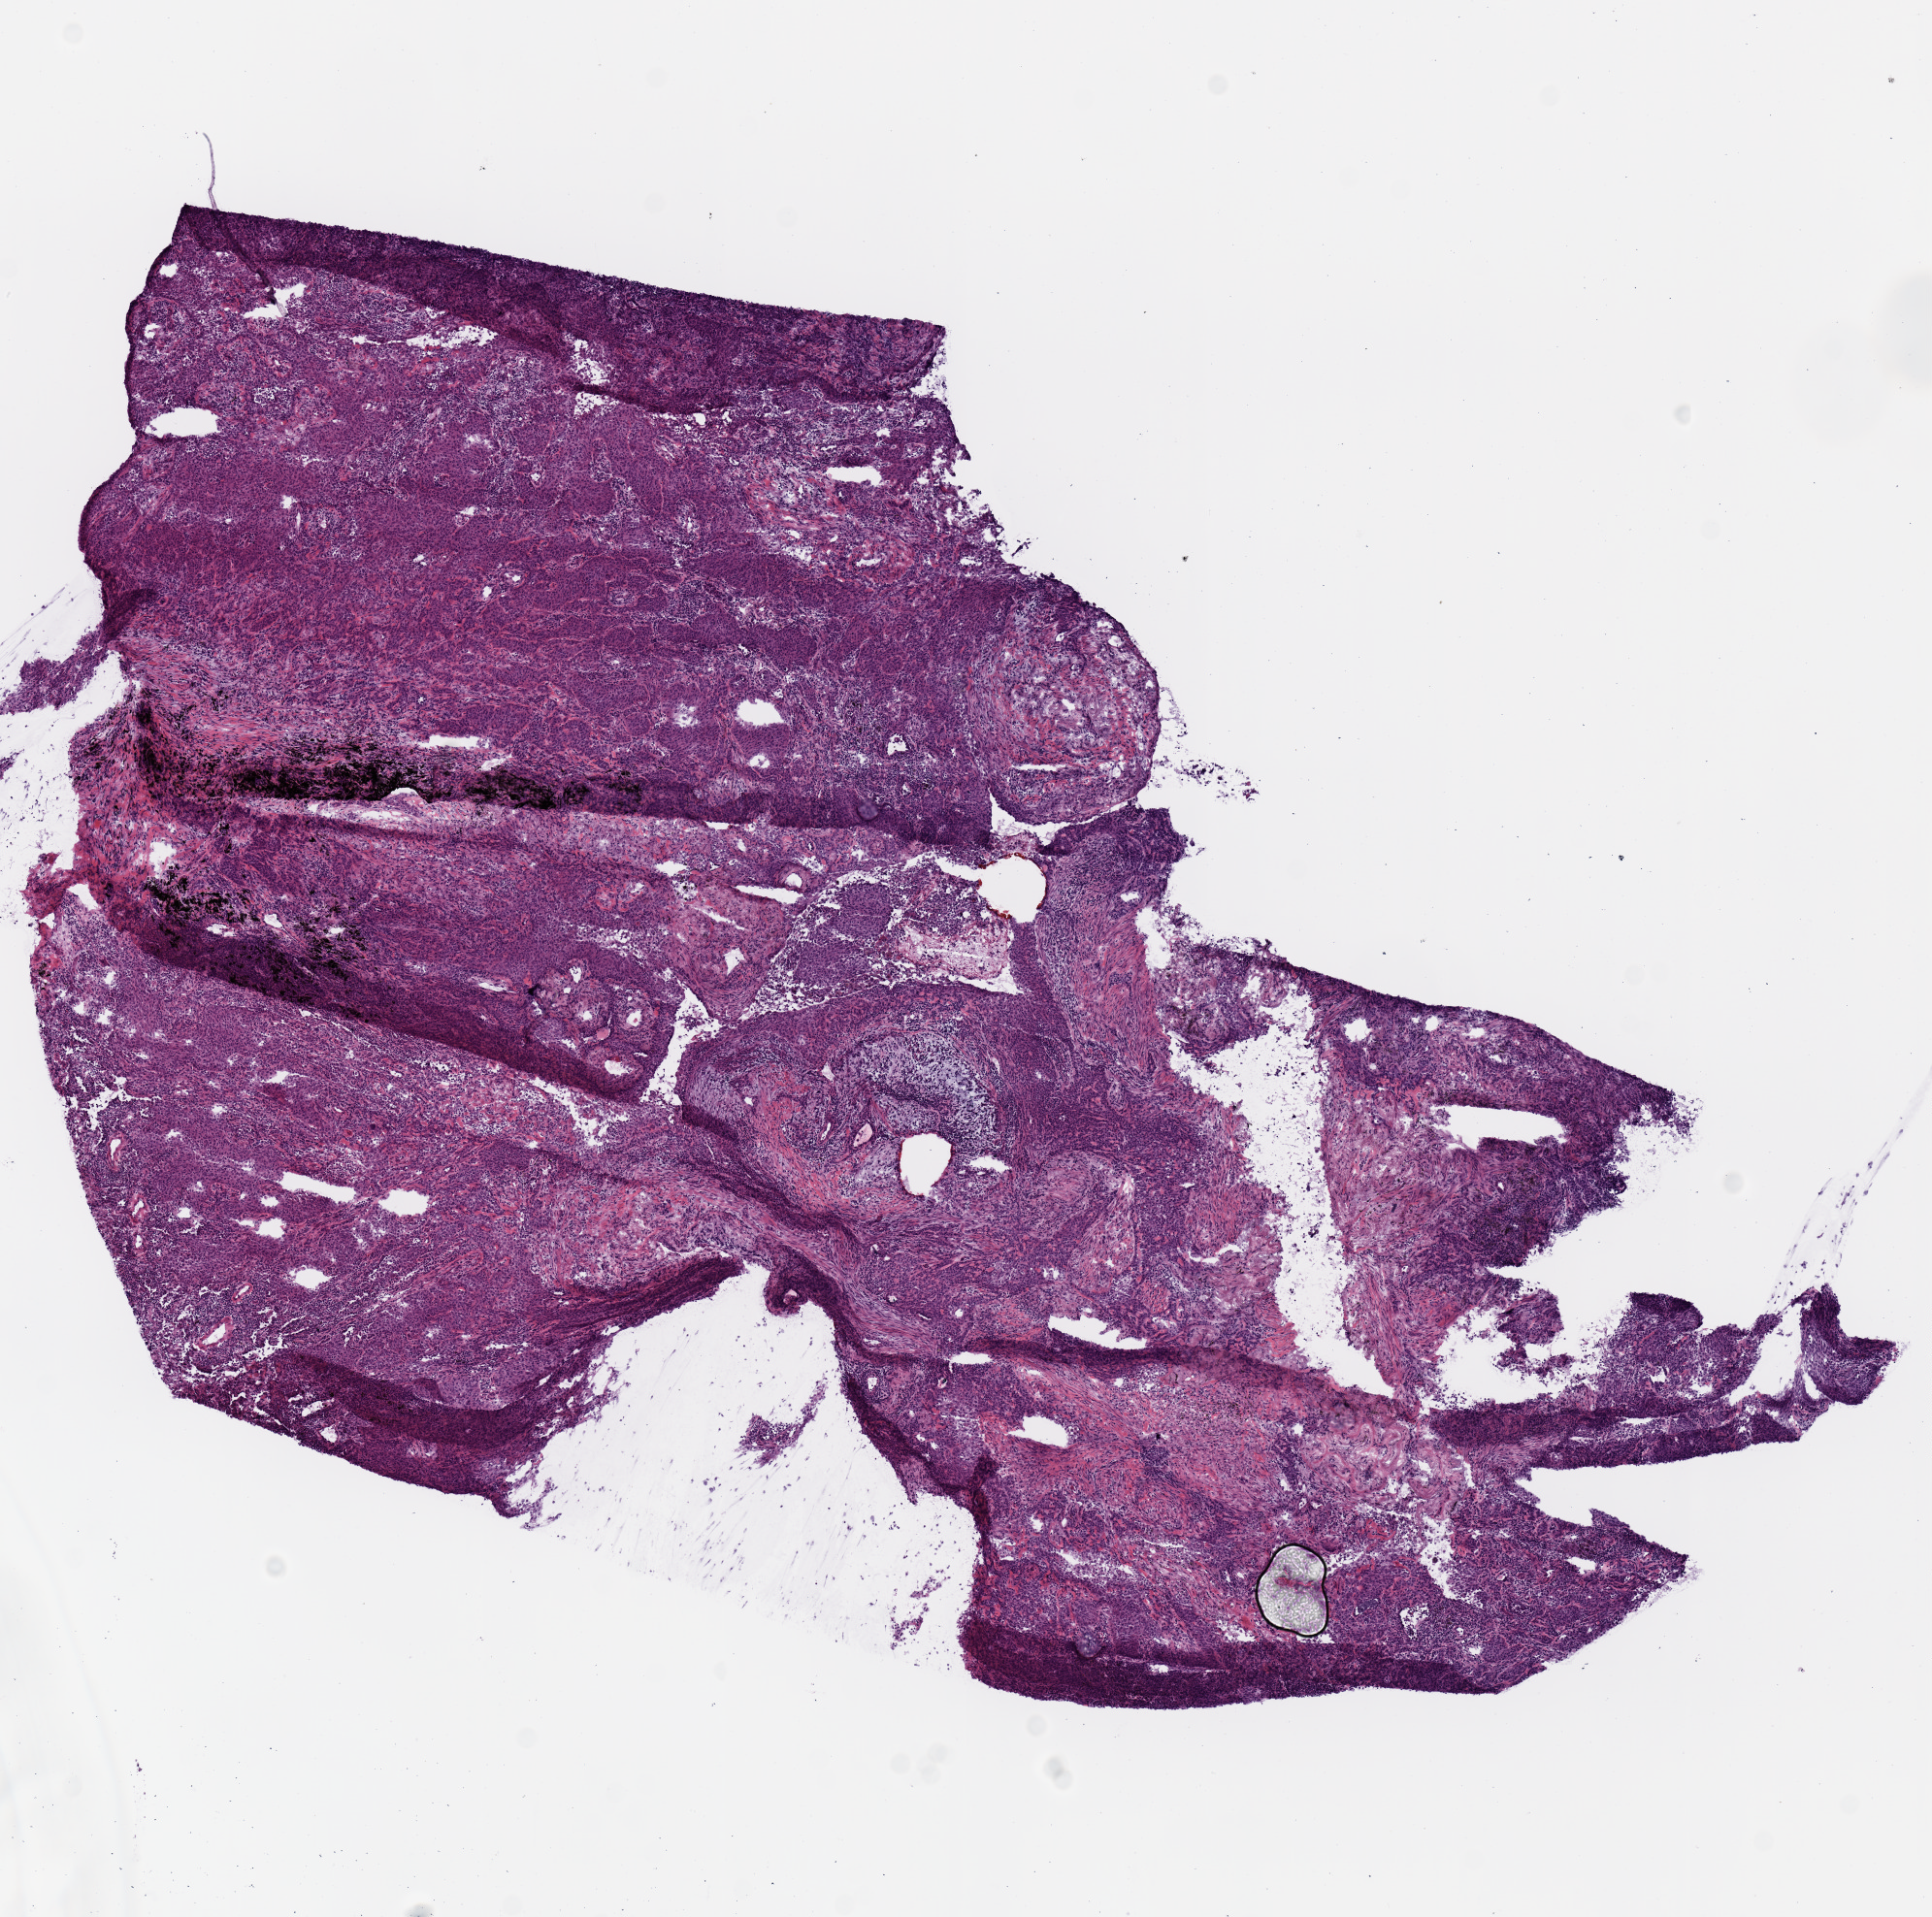
Digitized Hematoxylin and eosin (H&E) stained tissue section (whole slide), low-resolution overview of the scanned area, about 7.9 x 7.8 mm. Frozen section. Primary tumour sample from the lung. Male patient; age at initial diagnosis 66 years. Pathologist review of this section (percent, as recorded): tumour cells 80%, tumour nuclei 70%, normal cells 0%, stromal cells 20%, necrosis 0%. Inflammatory infiltration, as recorded: lymphocyte infiltration 20%, monocyte infiltration 20%, neutrophil infiltration 0%.
• histologic diagnosis: Squamous cell carcinoma, NOS (lower lobe, lung)
• TNM: T1b N0 MX
• AJCC pathologic stage: IA (7th edition)